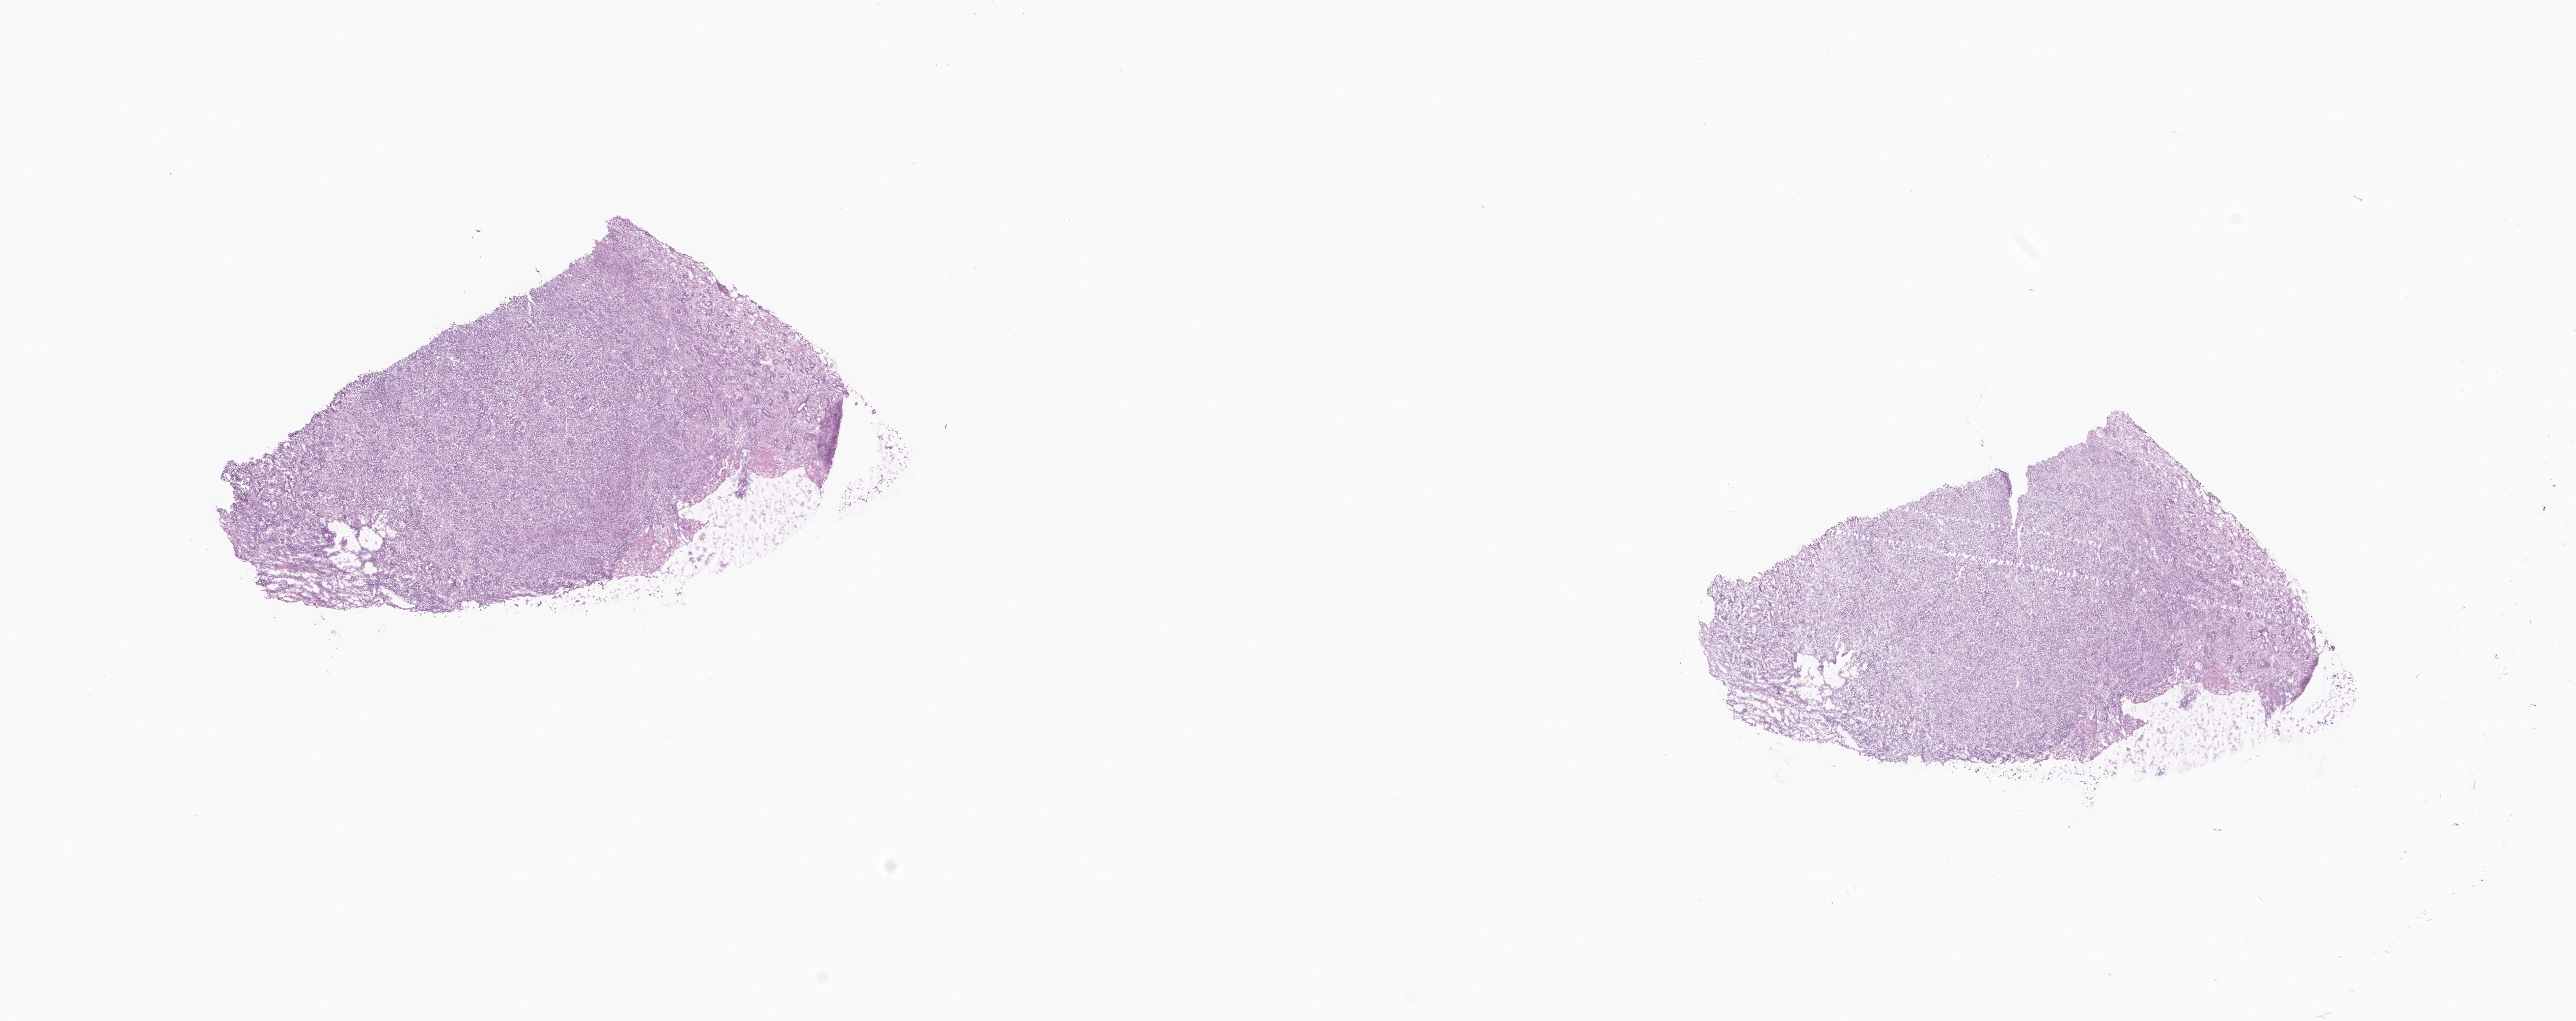
Hematoxylin and eosin (H&E) whole-slide image, whole scanned area (about 22.1 x 8.8 mm) shown as a low-resolution overview, frozen section (tissue freezing medium), specimen: metastatic tumor tissue, resected from adrenal gland. Female patient; age at initial diagnosis 65 years. Composition of this section per pathologist review: tumor cells 70%, tumor nuclei 70%, stromal cells 30%, necrosis 0%, normal cells 0%. Inflammatory infiltration, as recorded: lymphocyte infiltration 90%, monocyte infiltration 0%, neutrophil infiltration 0%.
Patient diagnosis (primary): Adenocarcinoma, NOS. Section: bottom of the tissue portion.